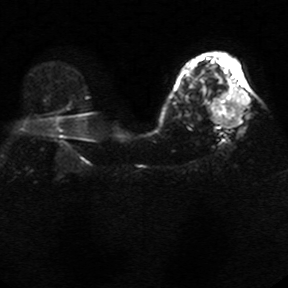
Breast MRI, one axial slice. Position 19 of 34 along the scan axis. Diffusion-weighted series; image 2 of 4 stored at this slice position (different b-values; order by instance number). 1.5 T. 5 mm slice thickness. 288 × 288 image matrix. Female patient.
Annotated regions visible in this slice (expert manual segmentation):
- tumour on diffusion-weighted imaging: bounding box (x1, y1, x2, y2) in pixels: (208, 87, 249, 127)